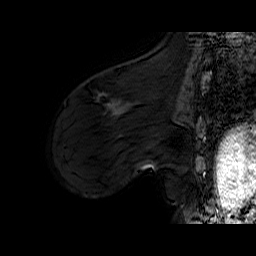
Breast MRI (dynamic contrast-enhanced), one sagittal slice. Slice 22 of 60 in the series (ordered by position). Dynamic contrast-enhanced series, time point 2 of 6 at this slice position (early post-contrast). 1.5 T. TE 6.4 ms, TR 32.9 ms. 4 mm slice thickness. 256 × 256 image matrix, field of view 200 × 200 mm. Female patient. Case-level facts recorded for this patient, not image findings: setting: breast cancer imaged before/during neoadjuvant chemotherapy; receptor status: HER2-positive.
Outlined on this slice (semi-automatic segmentation, software-assisted and operator-edited):
- analysis volume of interest (the breast-tissue region the enhancement analysis was run in; not a lesion): bounding box [x1, y1, x2, y2] px = [78, 94, 152, 149]
- tumour enhancement mask (voxels above the 100 % enhancement threshold inside the analysis volume of interest): [99, 95, 101, 97]